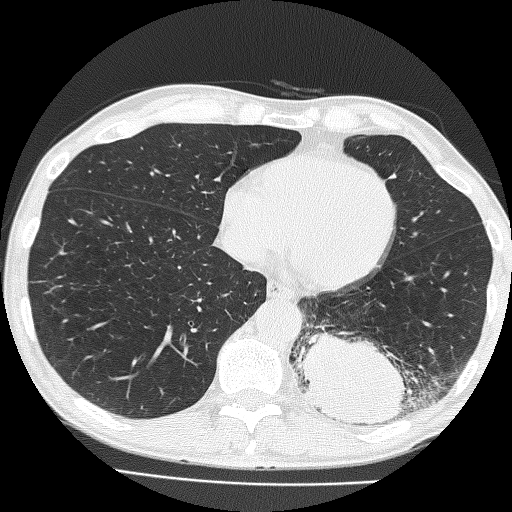
Low-dose screening chest CT, axial slice, baseline annual screen, lung window (W 1500 / L -600 HU), 2 mm slice thickness, lung (sharp) reconstruction kernel (FC51), slice 105 of 160 in the series, 512 × 512 image matrix. Male, age 58 years at enrolment. Current smoker at enrolment.
Expert reader's lesion annotation, bounding box <292,297,428,435> (left, top, right, bottom; pixels). The screening reader recorded 2 non-calcified nodules or masses ≥4 mm on this exam (left lower lobe, left upper lobe); which of them this box marks is not recorded. Official screen result: positive, change unspecified: nodule(s) >= 4 mm or enlarging nodule(s), mass(es), or other non-specific abnormalities suspicious for lung cancer. Lung cancer was diagnosed 39 days after this screen: non-small cell carcinoma, left lower lobe, poorly differentiated (G3), stage IV (AJCC 6th edition), 74 mm at pathology.